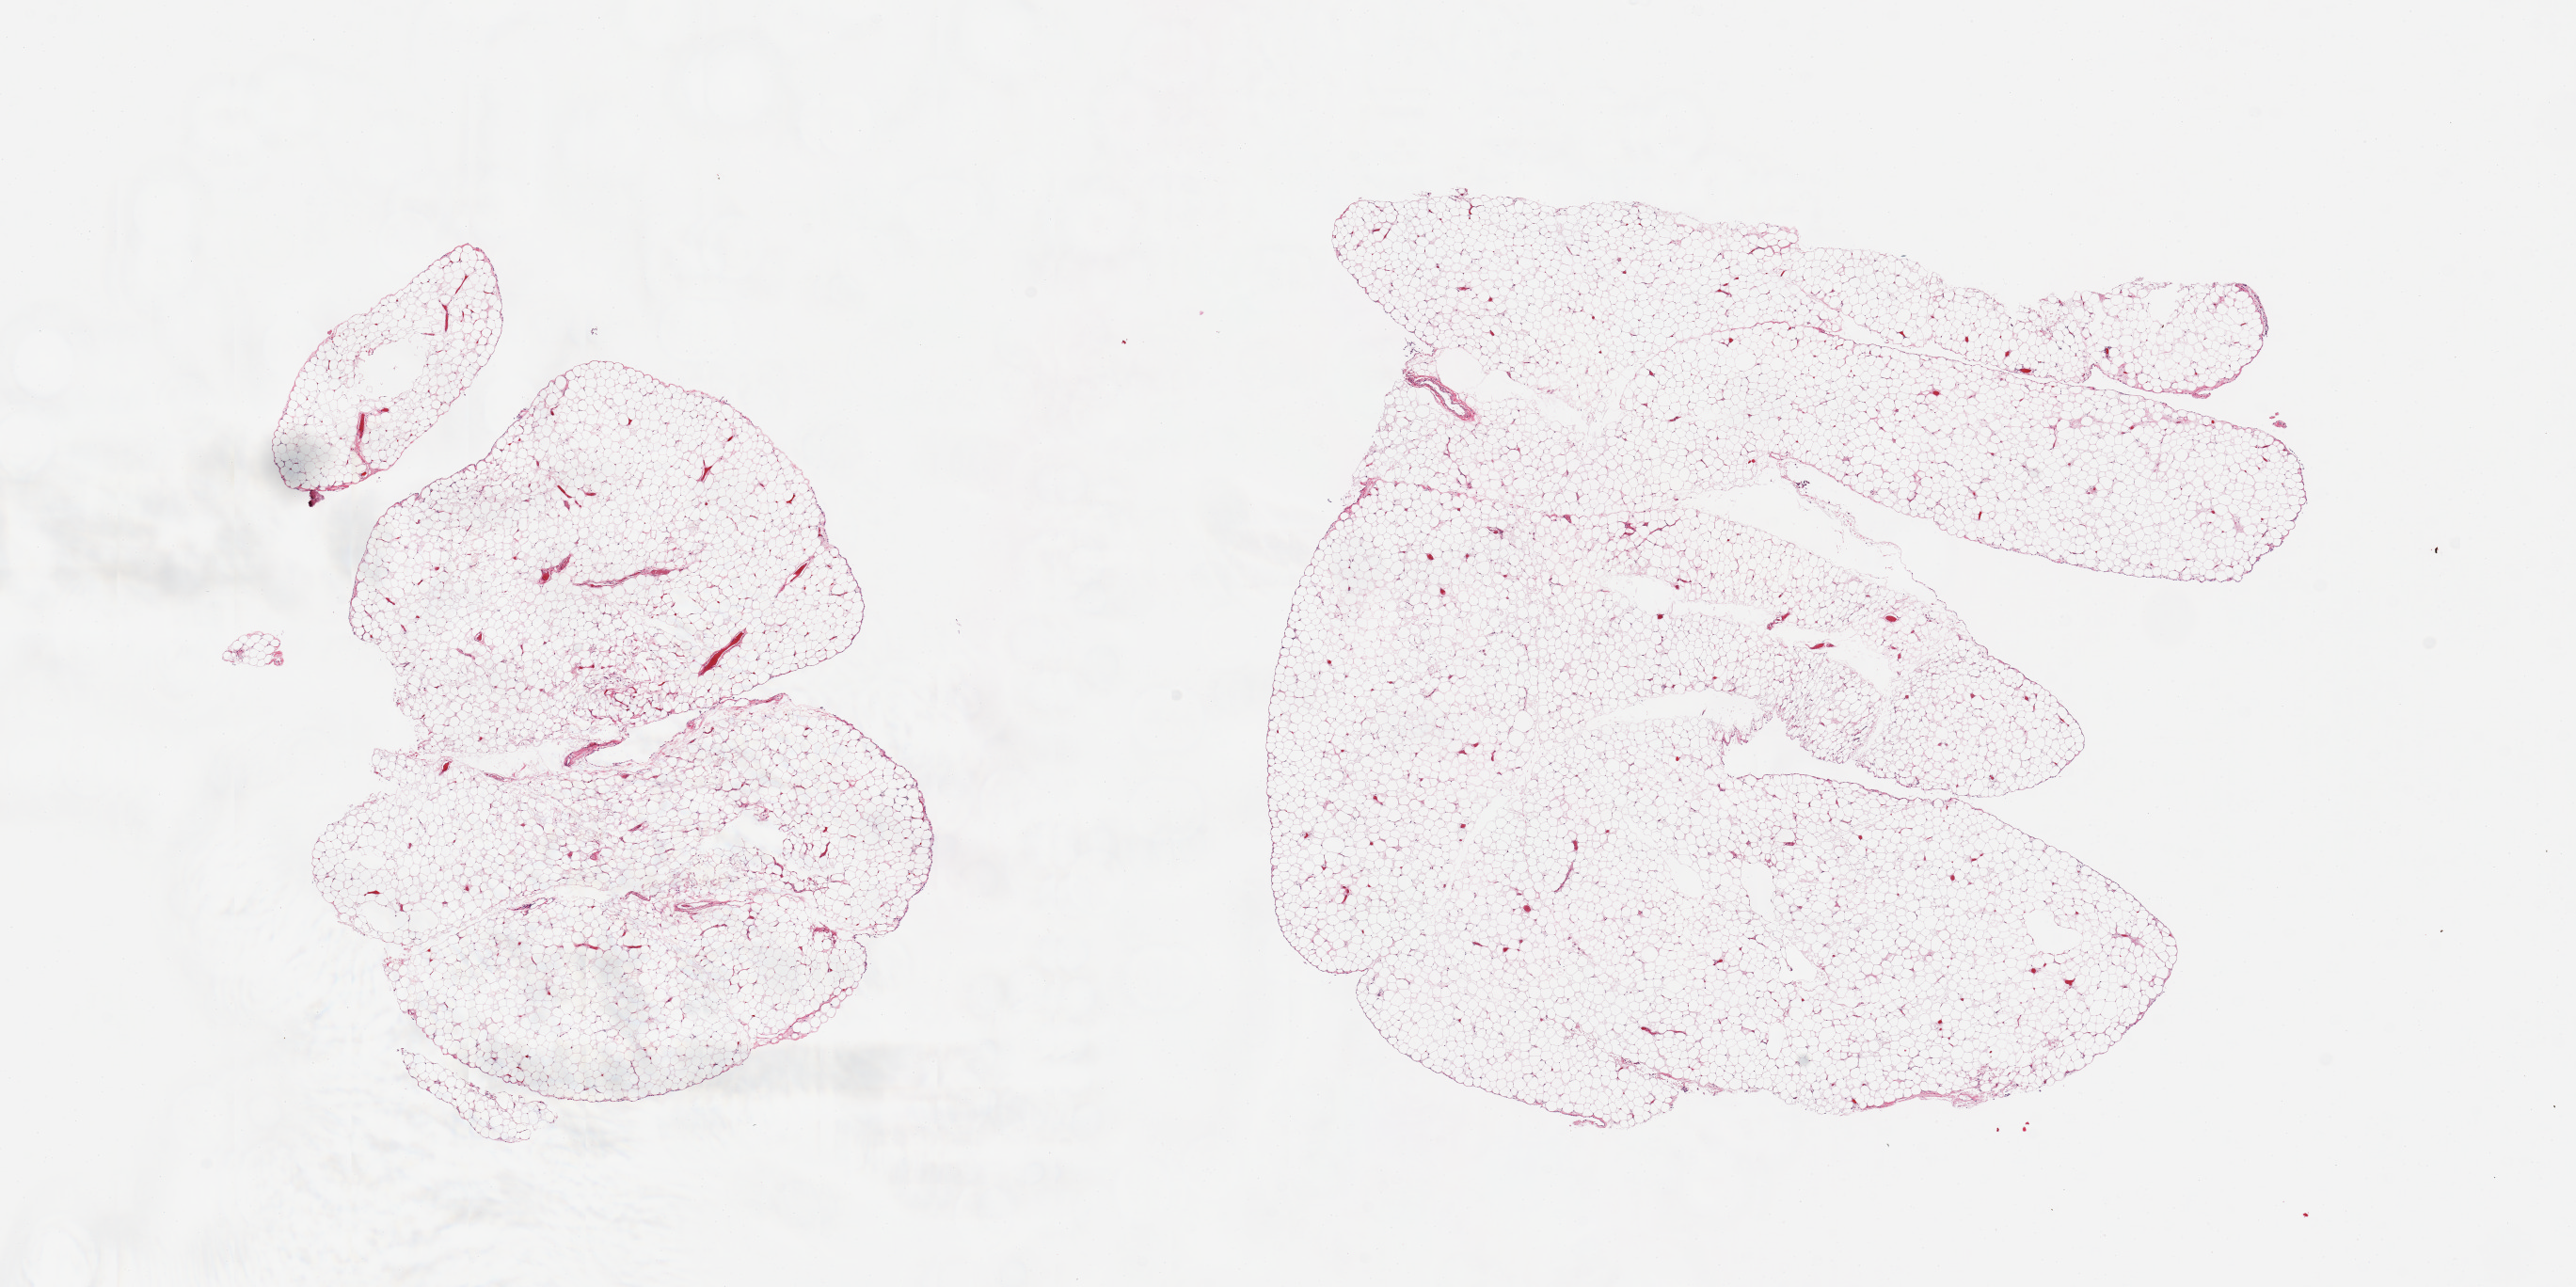
Digitized H&E-stained section, low-resolution overview of the scanned area, about 21.7 x 10.8 mm (acquisition: 20x scan); PAXgene-fixed paraffin-embedded (PFPE) section; sampled site (target tissue): omentum; donor tissue sample. Donor: male.
Reviewer comment on this tissue sample: 2 pieces, trace fascia.